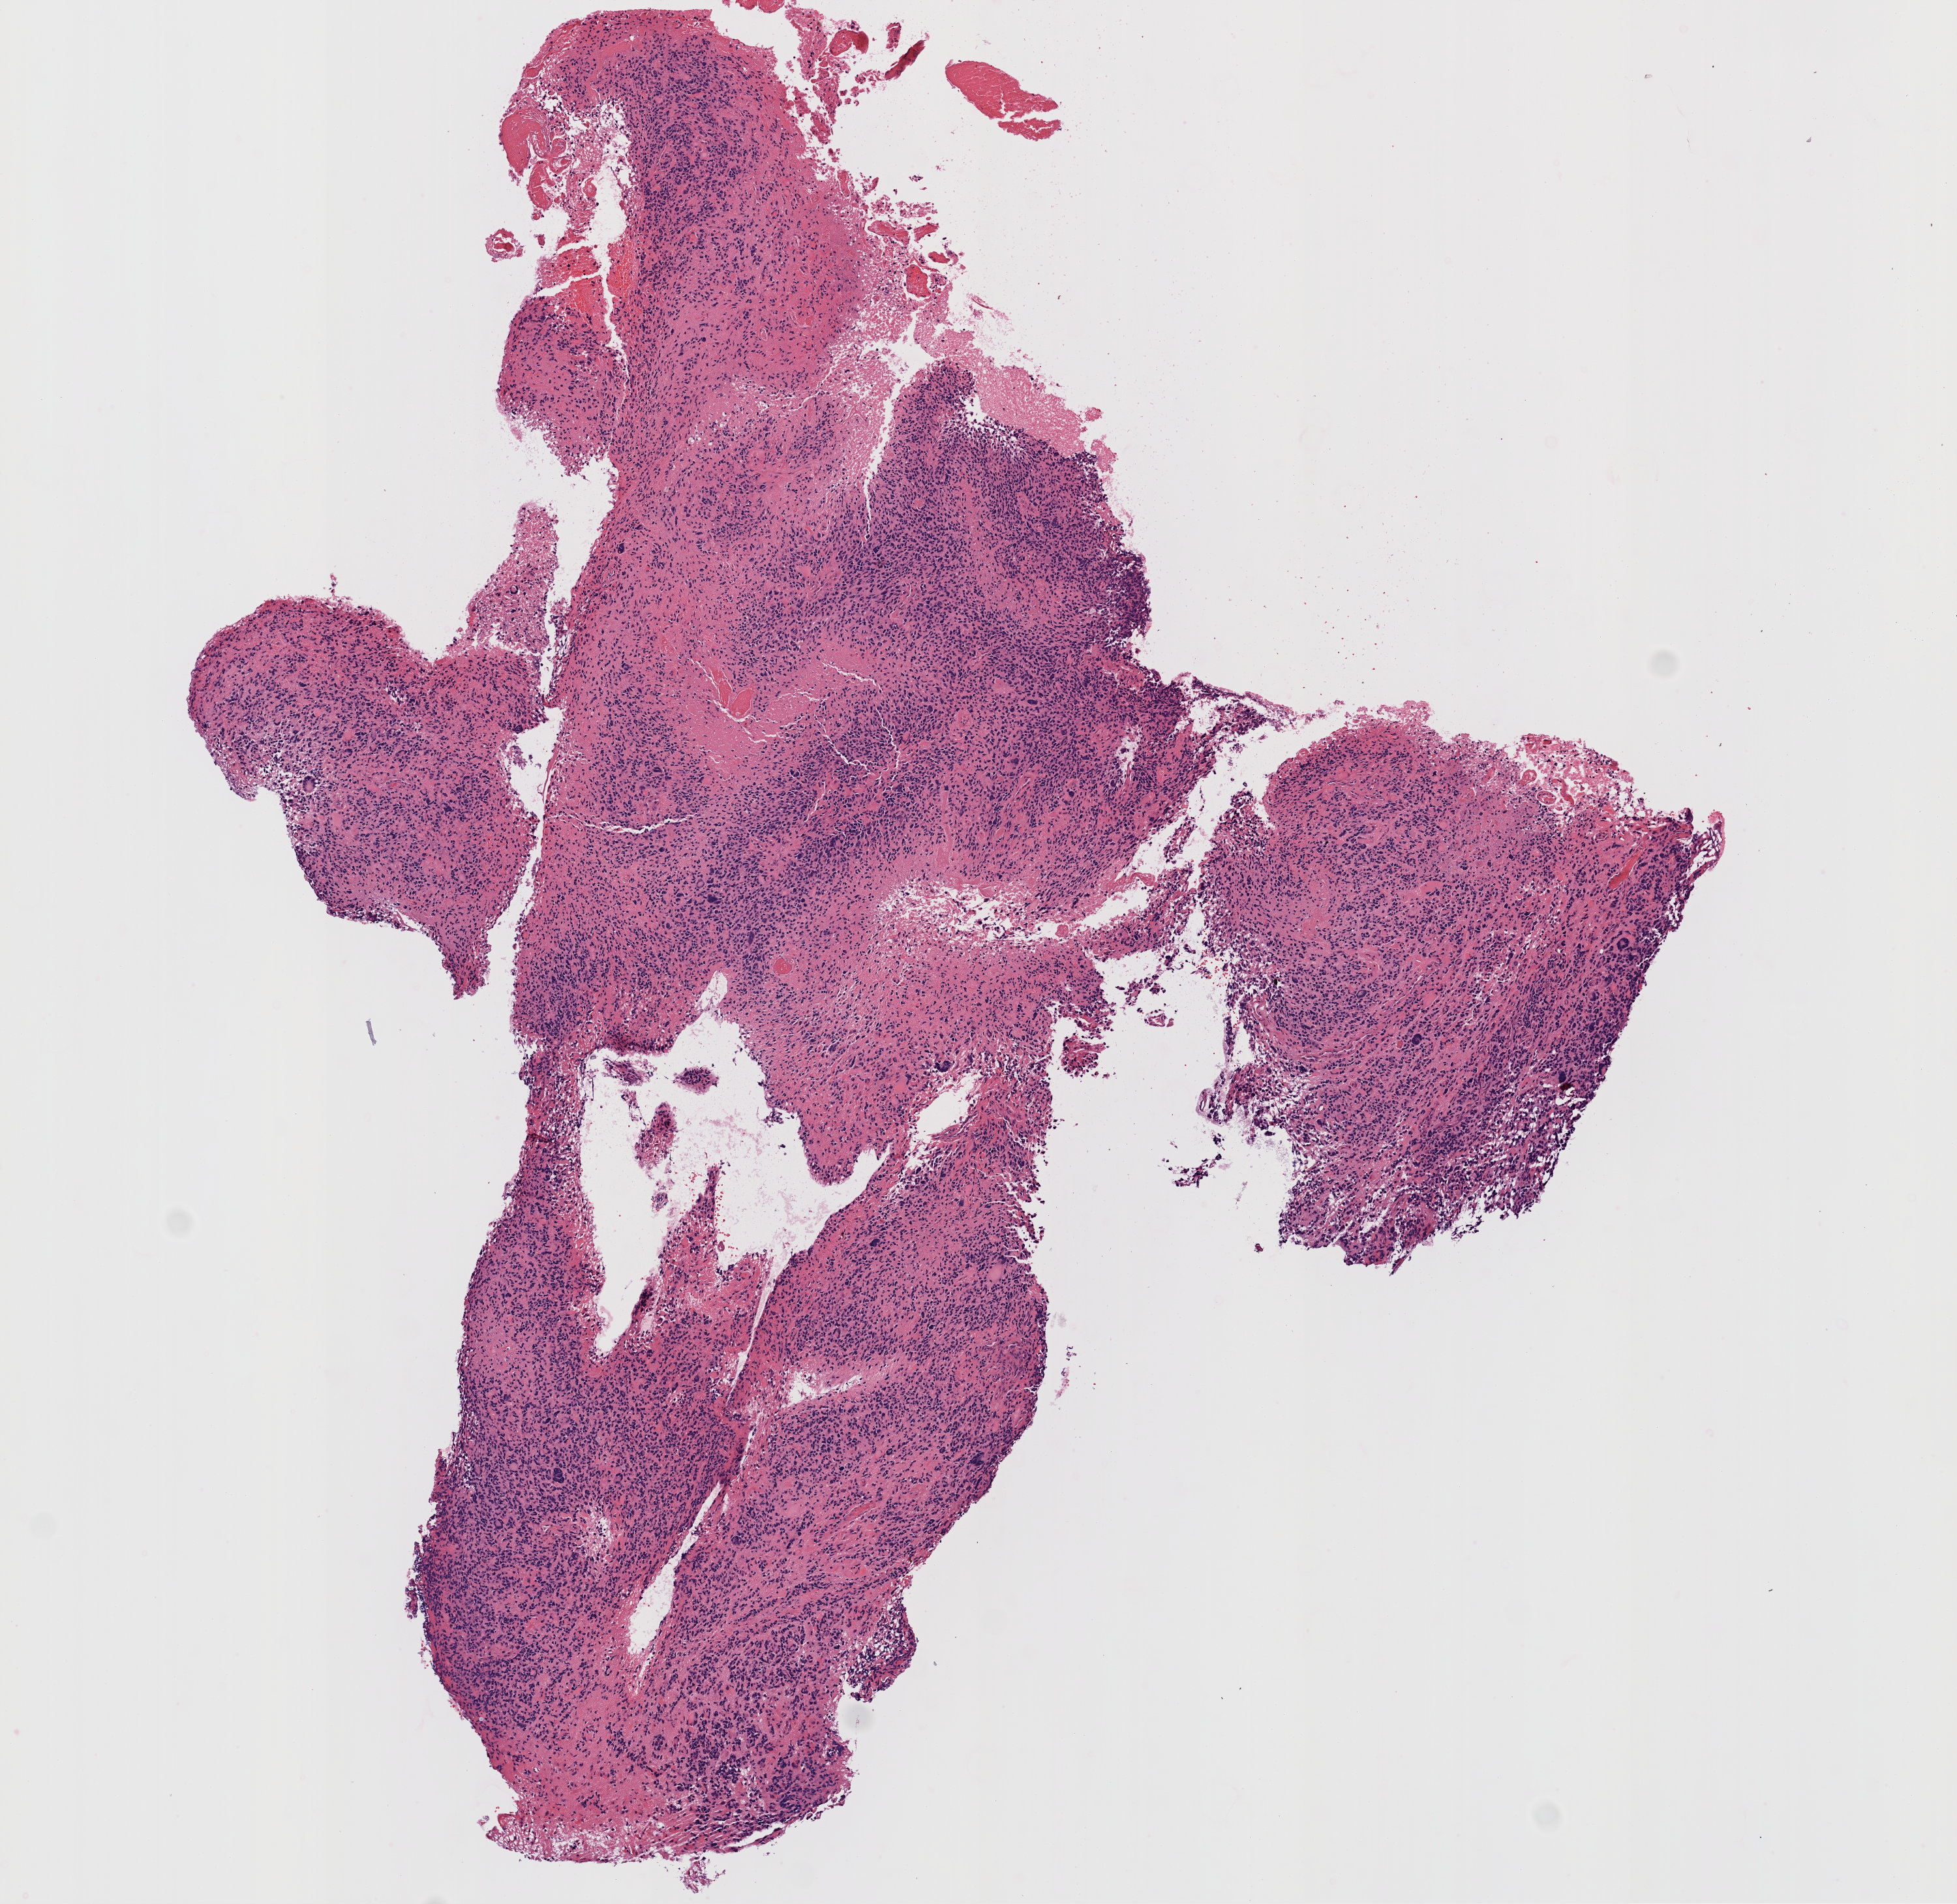
Whole-slide histology image, Hematoxylin and eosin (H&E) stained, low-resolution overview of the scanned area, about 6.0 x 5.9 mm (from a 20x scan); FFPE section; primary tumour sample from the brain. Female, age 72 years at initial diagnosis.
Histologic diagnosis: Glioblastoma.